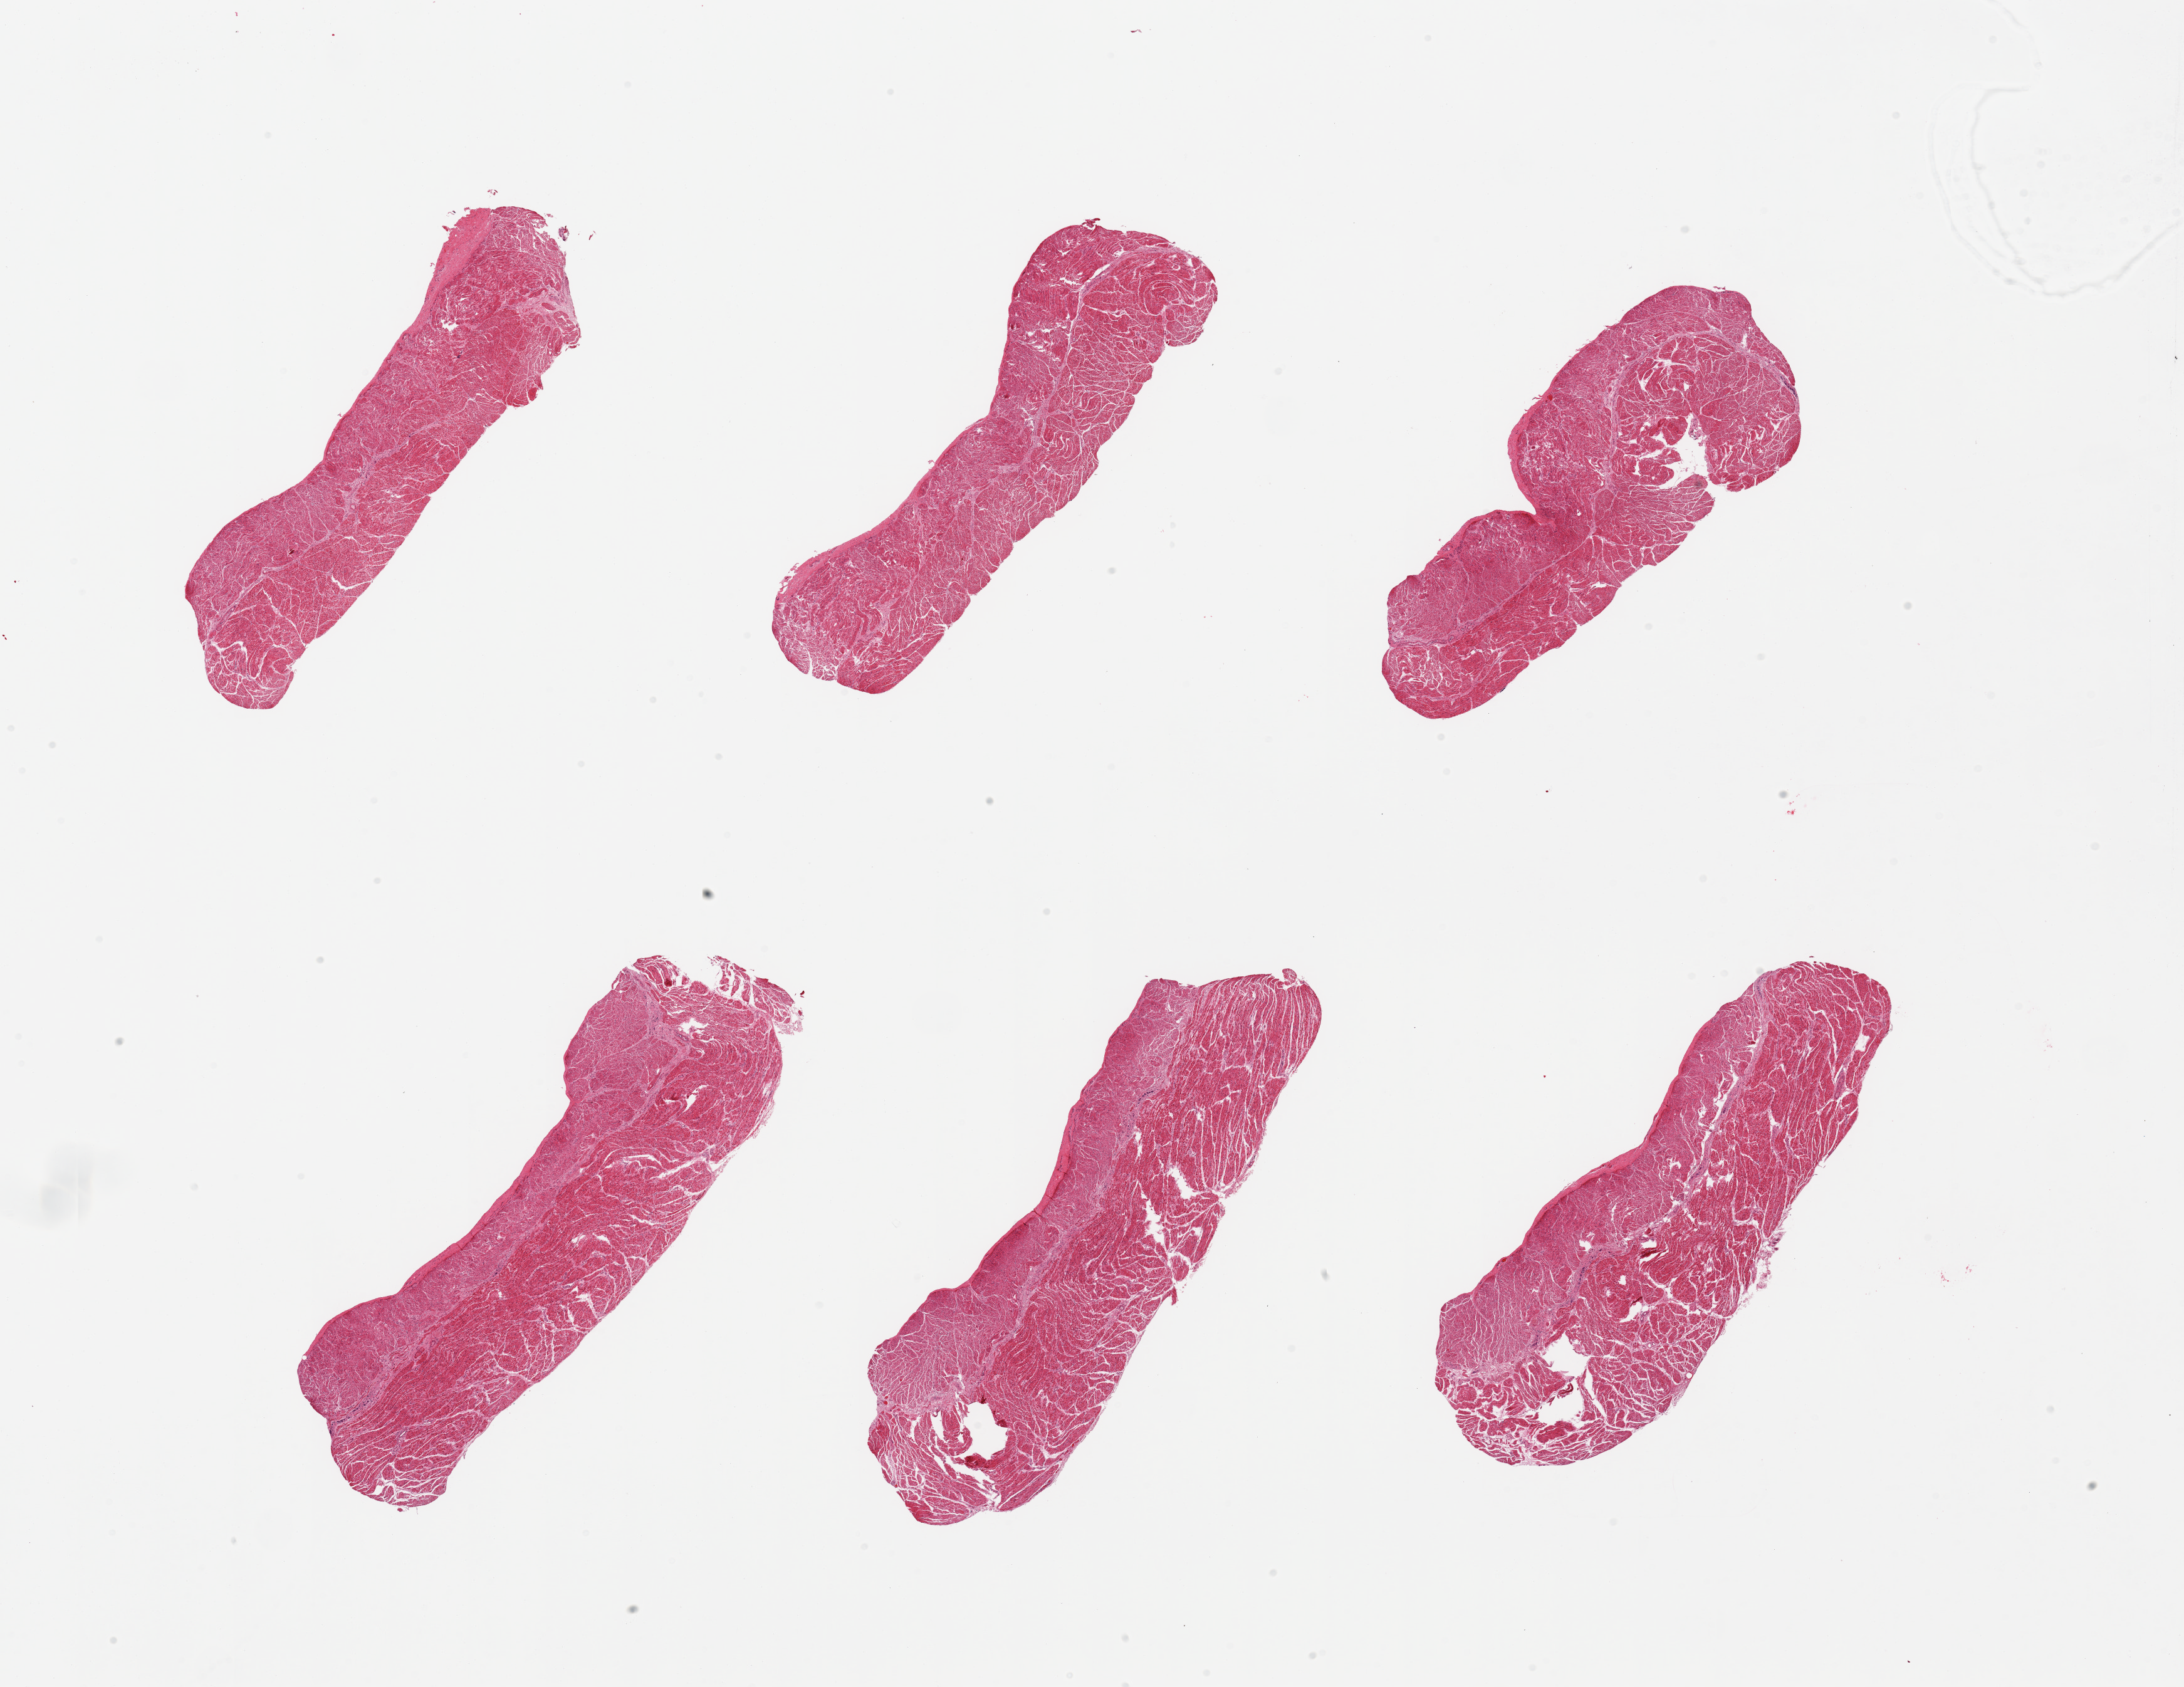
Whole-slide image, H&E stain, brightfield, a low-resolution overview of the entire scanned area, about 27.6 x 21.3 mm (acquisition: 20x scan). PAXgene-fixed paraffin-embedded (PFPE) section. Target tissue: esophageal muscle. Donor tissue sample. Male donor.
Review note (as recorded): 6 pieces, target muscularis.